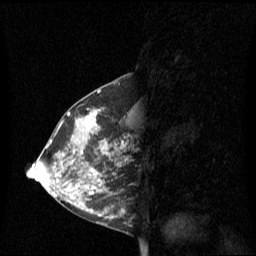
Breast MRI (dynamic contrast-enhanced), one sagittal slice. Position 30 of 60 along the scan axis. Dynamic contrast-enhanced series, image 2 of 3 at this slice position (ordered by acquisition). 1.5 T. TE 4.2 ms, TR 8.4 ms. 256 × 256 image matrix, field of view 240 × 240 mm. Patient: female, 42 years. From the clinical record (not read from this slice): setting: breast cancer imaged before/during neoadjuvant chemotherapy; receptor status: HR-positive, HER2-negative.
Structures marked on this image (semi-automatically segmented with operator editing):
- analysis volume of interest (the breast-tissue region the enhancement analysis was run in; not a lesion): bounding box [x1, y1, x2, y2] px = [68, 108, 129, 201]
- tumour enhancement mask (voxels above the 70 % enhancement threshold inside the analysis volume of interest): [82, 110, 125, 195]